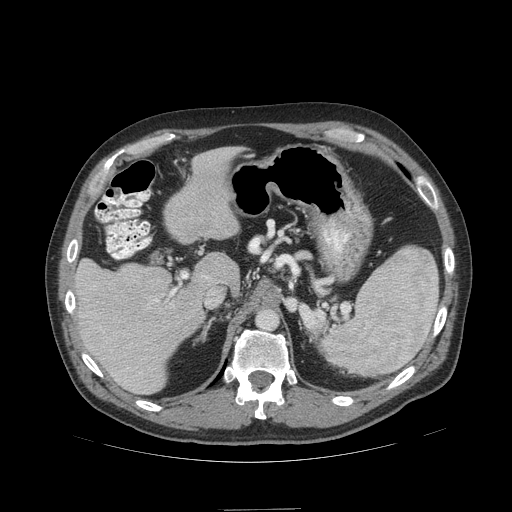
Contrast-enhanced abdominal CT (liver protocol), one axial slice; reconstruction kernel STANDARD; 140 kVp; soft-tissue window (W 400 / L 40 HU); 2.5 mm slice thickness; 512 × 512 image matrix, field of view 440 × 440 mm. Case-level facts recorded for this patient, not image findings: diagnosis: hepatocellular carcinoma (patient treated with transarterial chemoembolisation; whether this scan precedes or follows treatment is not stated here); TNM stage (as recorded): Stage-I; Child-Pugh class: A; tumour nodularity: uninodular.
Annotated regions visible in this slice (semi-automatically segmented with operator editing):
- liver parenchyma outside the tumour (the mass and vessels are separate outlines, so this box may not span the whole liver): bounding box <72,148,238,394> (left, top, right, bottom; pixels)
- liver vessels: <110,275,211,351>